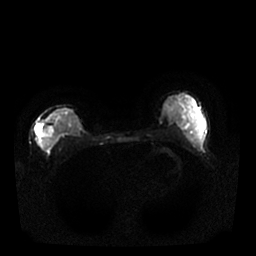
Breast MRI, one axial slice; slice 14 of 25 in the series (ordered by position); diffusion-weighted series; image 2 of 4 stored at this slice position (different b-values; order by instance number); 1.5 T; 256 × 256 image matrix, field of view 340 × 340 mm. Female patient.
Outlined on this slice (outlined manually by an expert reader):
- tumour on diffusion-weighted imaging: bounding box [x1, y1, x2, y2] px = [36, 123, 56, 151]